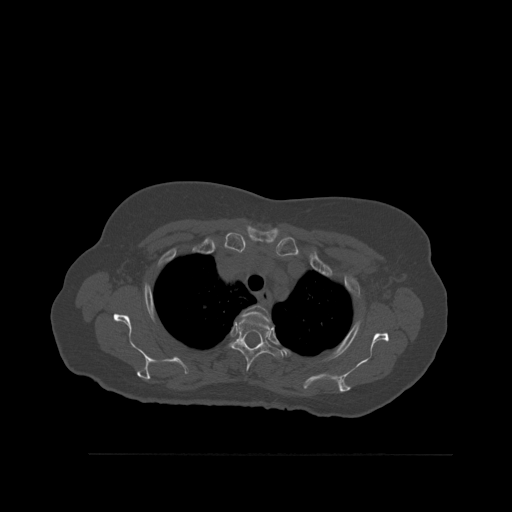
CT including the spine, one axial slice; position 421 of 527 along the scan axis; bone window (W 1800 / L 400 HU); 512 × 512 image matrix, field of view 470 × 470 mm. Female patient, age 73 years. Case-level facts recorded for this patient, not image findings: primary cancer: breast.
Outlined on this slice (semi-automatically segmented with operator editing):
- T2 vertebra: bounding box [x1, y1, x2, y2] px = [241, 305, 271, 322]
- T3 vertebra: [230, 315, 283, 373]